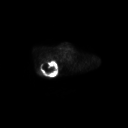
FDG PET of an extremity soft-tissue mass (from a PET/CT study), one axial slice. Slice 214 of 267 in the series (ordered by position). 128 × 128 image matrix. Patient: male, 61 years. Case-level facts recorded for this patient, not image findings: histological type: pleiomorphic spindle cell undifferentiated; grade: high; site of the primary tumour: right parascapusular.
Structures marked on this image (expert contour drawn on MRI and transferred to this co-registered scan by the dataset authors):
- gross tumour volume including surrounding oedema: bounding box <37,60,60,76> (left, top, right, bottom; pixels)
- gross tumour volume (mass): <41,61,56,75>